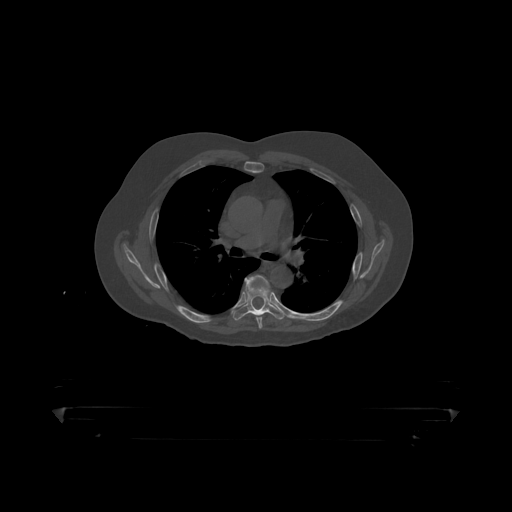
CT including the spine, one axial slice; slice 307 of 390 in the series (ordered by position); reconstruction kernel STANDARD; 120 kVp; bone window (W 1800 / L 400 HU); 1.25 mm slice thickness; 512 × 512 image matrix, field of view 650 × 650 mm. Patient: male, 60 years. Case-level facts recorded for this patient, not image findings: primary cancer: prostate.
Outlined on this slice (semi-automatic segmentation, software-assisted and operator-edited):
- T5 vertebra: bounding box (x1, y1, x2, y2) in pixels: (257, 318, 263, 319)
- T6 vertebra: (234, 276, 283, 318)